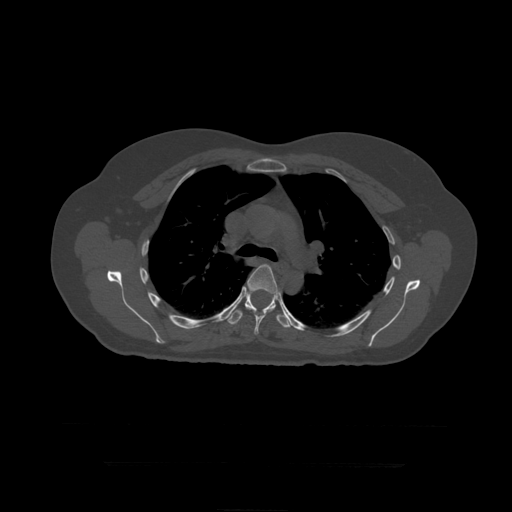
CT including the spine, one axial slice. Slice 312 of 399 in the series (ordered by position). Bone window (W 1800 / L 400 HU). 1.25 mm slice thickness. 512 × 512 image matrix. Patient age 41 years. Case-level facts recorded for this patient, not image findings: primary cancer: breast.
Outlined on this slice (semi-automatic segmentation, software-assisted and operator-edited):
- T6 vertebra: bounding box [x1, y1, x2, y2] px = [245, 264, 278, 335]
- T7 vertebra: [226, 291, 291, 328]